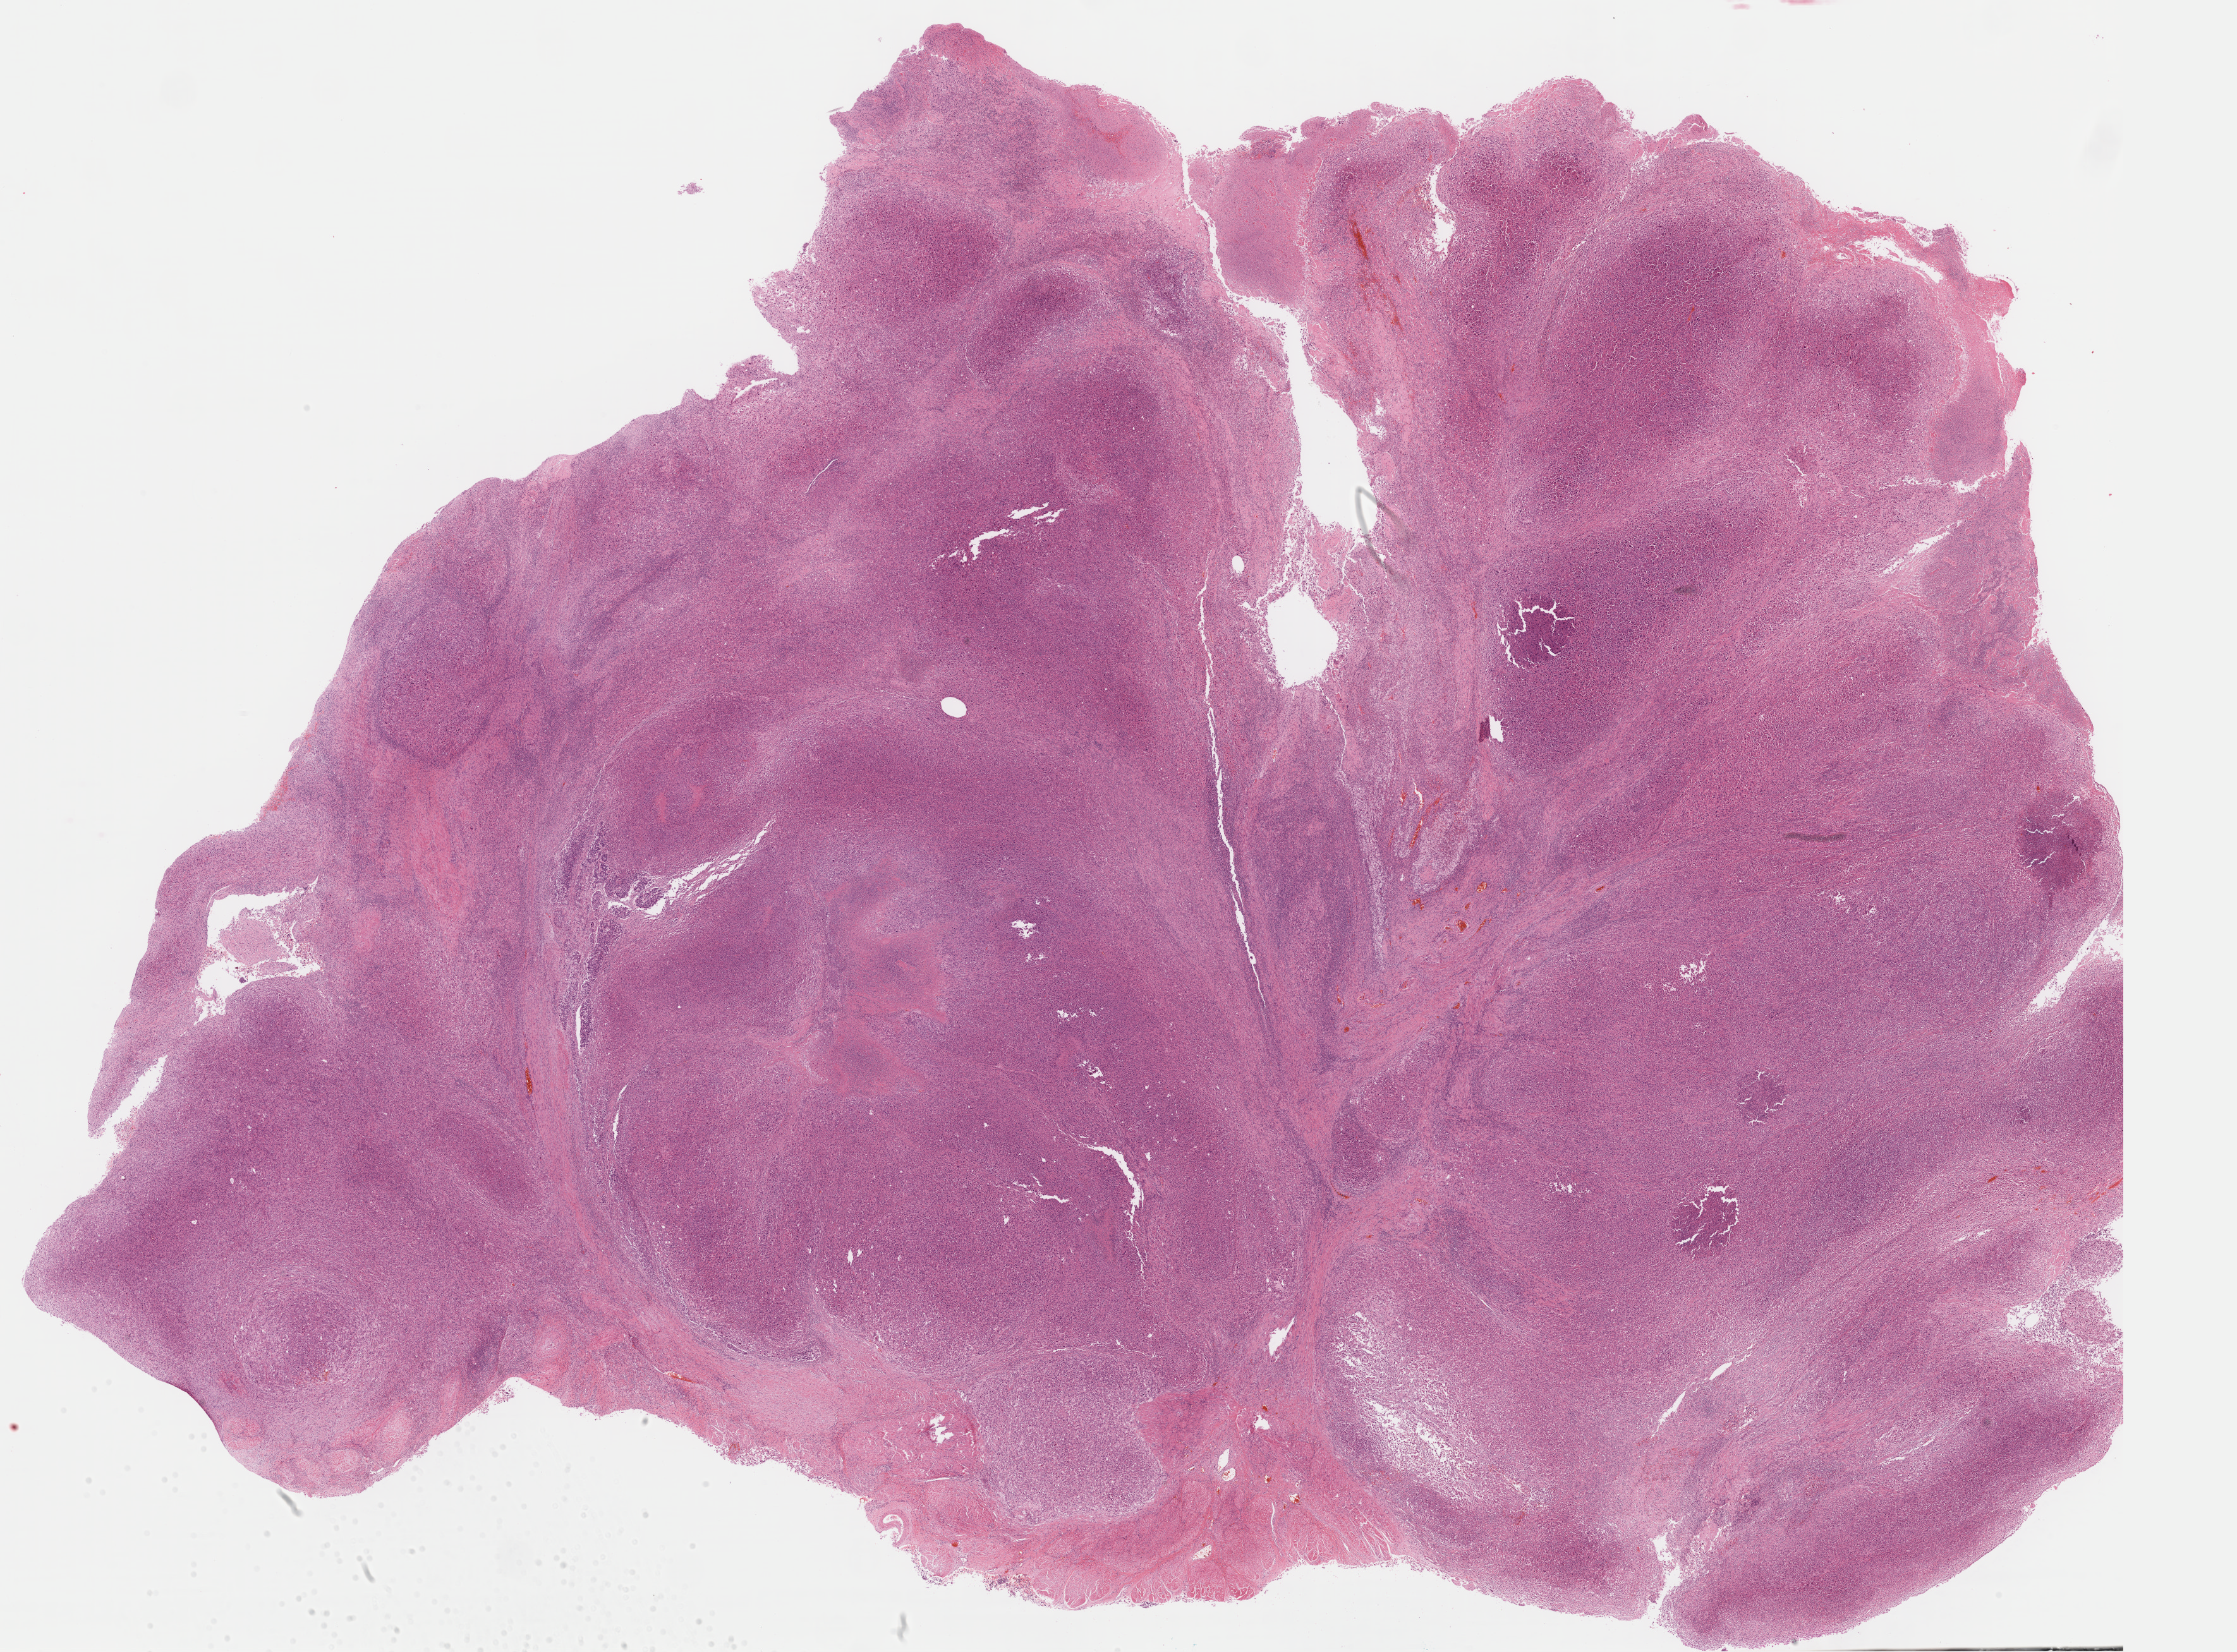
Digitized H&E-stained tissue section (whole slide) — whole scanned area (about 28.0 x 20.7 mm, acquisition: 40x scan) shown as a low-resolution overview, formalin-fixed paraffin-embedded (FFPE) diagnostic section, sample: primary tumour, bladder. Male patient; age at initial diagnosis 44 years.
Diagnosis: Papillary transitional cell carcinoma.